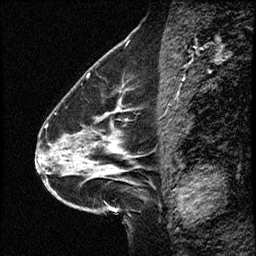
Breast MRI (dynamic contrast-enhanced), one sagittal slice. Slice 25 of 50 in the series (ordered by position). Dynamic contrast-enhanced study with each time point stored as its own series, time point 2 of 4 at this slice position (early post-contrast, ordered by acquisition time). 1.5 T. TE 4.2 ms, TR 17.5 ms. 3 mm slice thickness. 256 × 256 image matrix, field of view 200 × 200 mm. From the clinical record (not read from this slice): setting: breast cancer imaged before/during neoadjuvant chemotherapy.
Annotated regions visible in this slice (semi-automatically segmented with operator editing):
- analysis volume of interest (the breast-tissue region the enhancement analysis was run in; not a lesion): bounding box (x1, y1, x2, y2) in pixels: (52, 98, 158, 207)
- tumour enhancement mask (voxels above the 100 % enhancement threshold inside the analysis volume of interest): (76, 99, 121, 172)